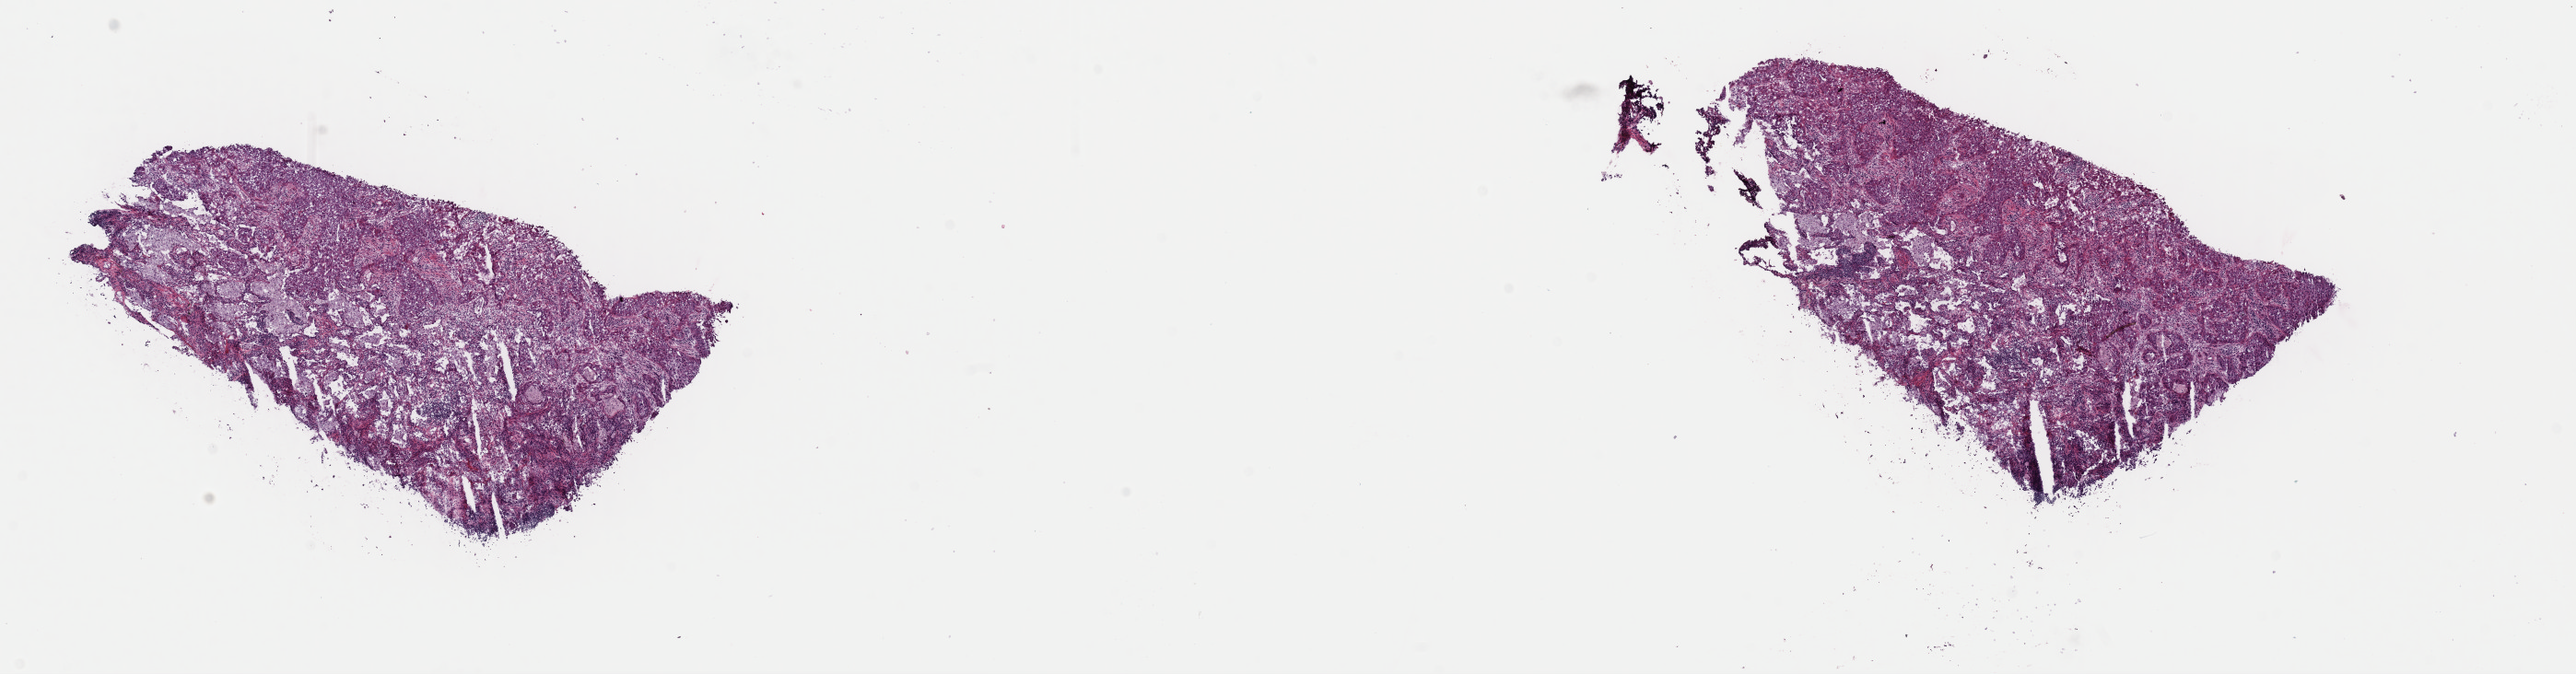
Whole-slide histology image, Hematoxylin and eosin (H&E) stained — whole scanned area (about 22.1 x 5.8 mm) shown as a low-resolution overview. Frozen section from the top of the tissue portion. Lung, primary tumour sample. Male, age 47 years at initial diagnosis. Composition of this section per pathologist review: tumour cells 60%, tumour nuclei 60%, normal cells 10%, stromal cells 30%, necrosis 0%. Infiltration values recorded for this section: lymphocyte infiltration 7%, monocyte infiltration 5%, neutrophil infiltration 0%.
Laterality: right. TNM: T2b N0 M0. Diagnosis: Squamous cell carcinoma, NOS (upper lobe, lung). AJCC pathologic stage: IIA.